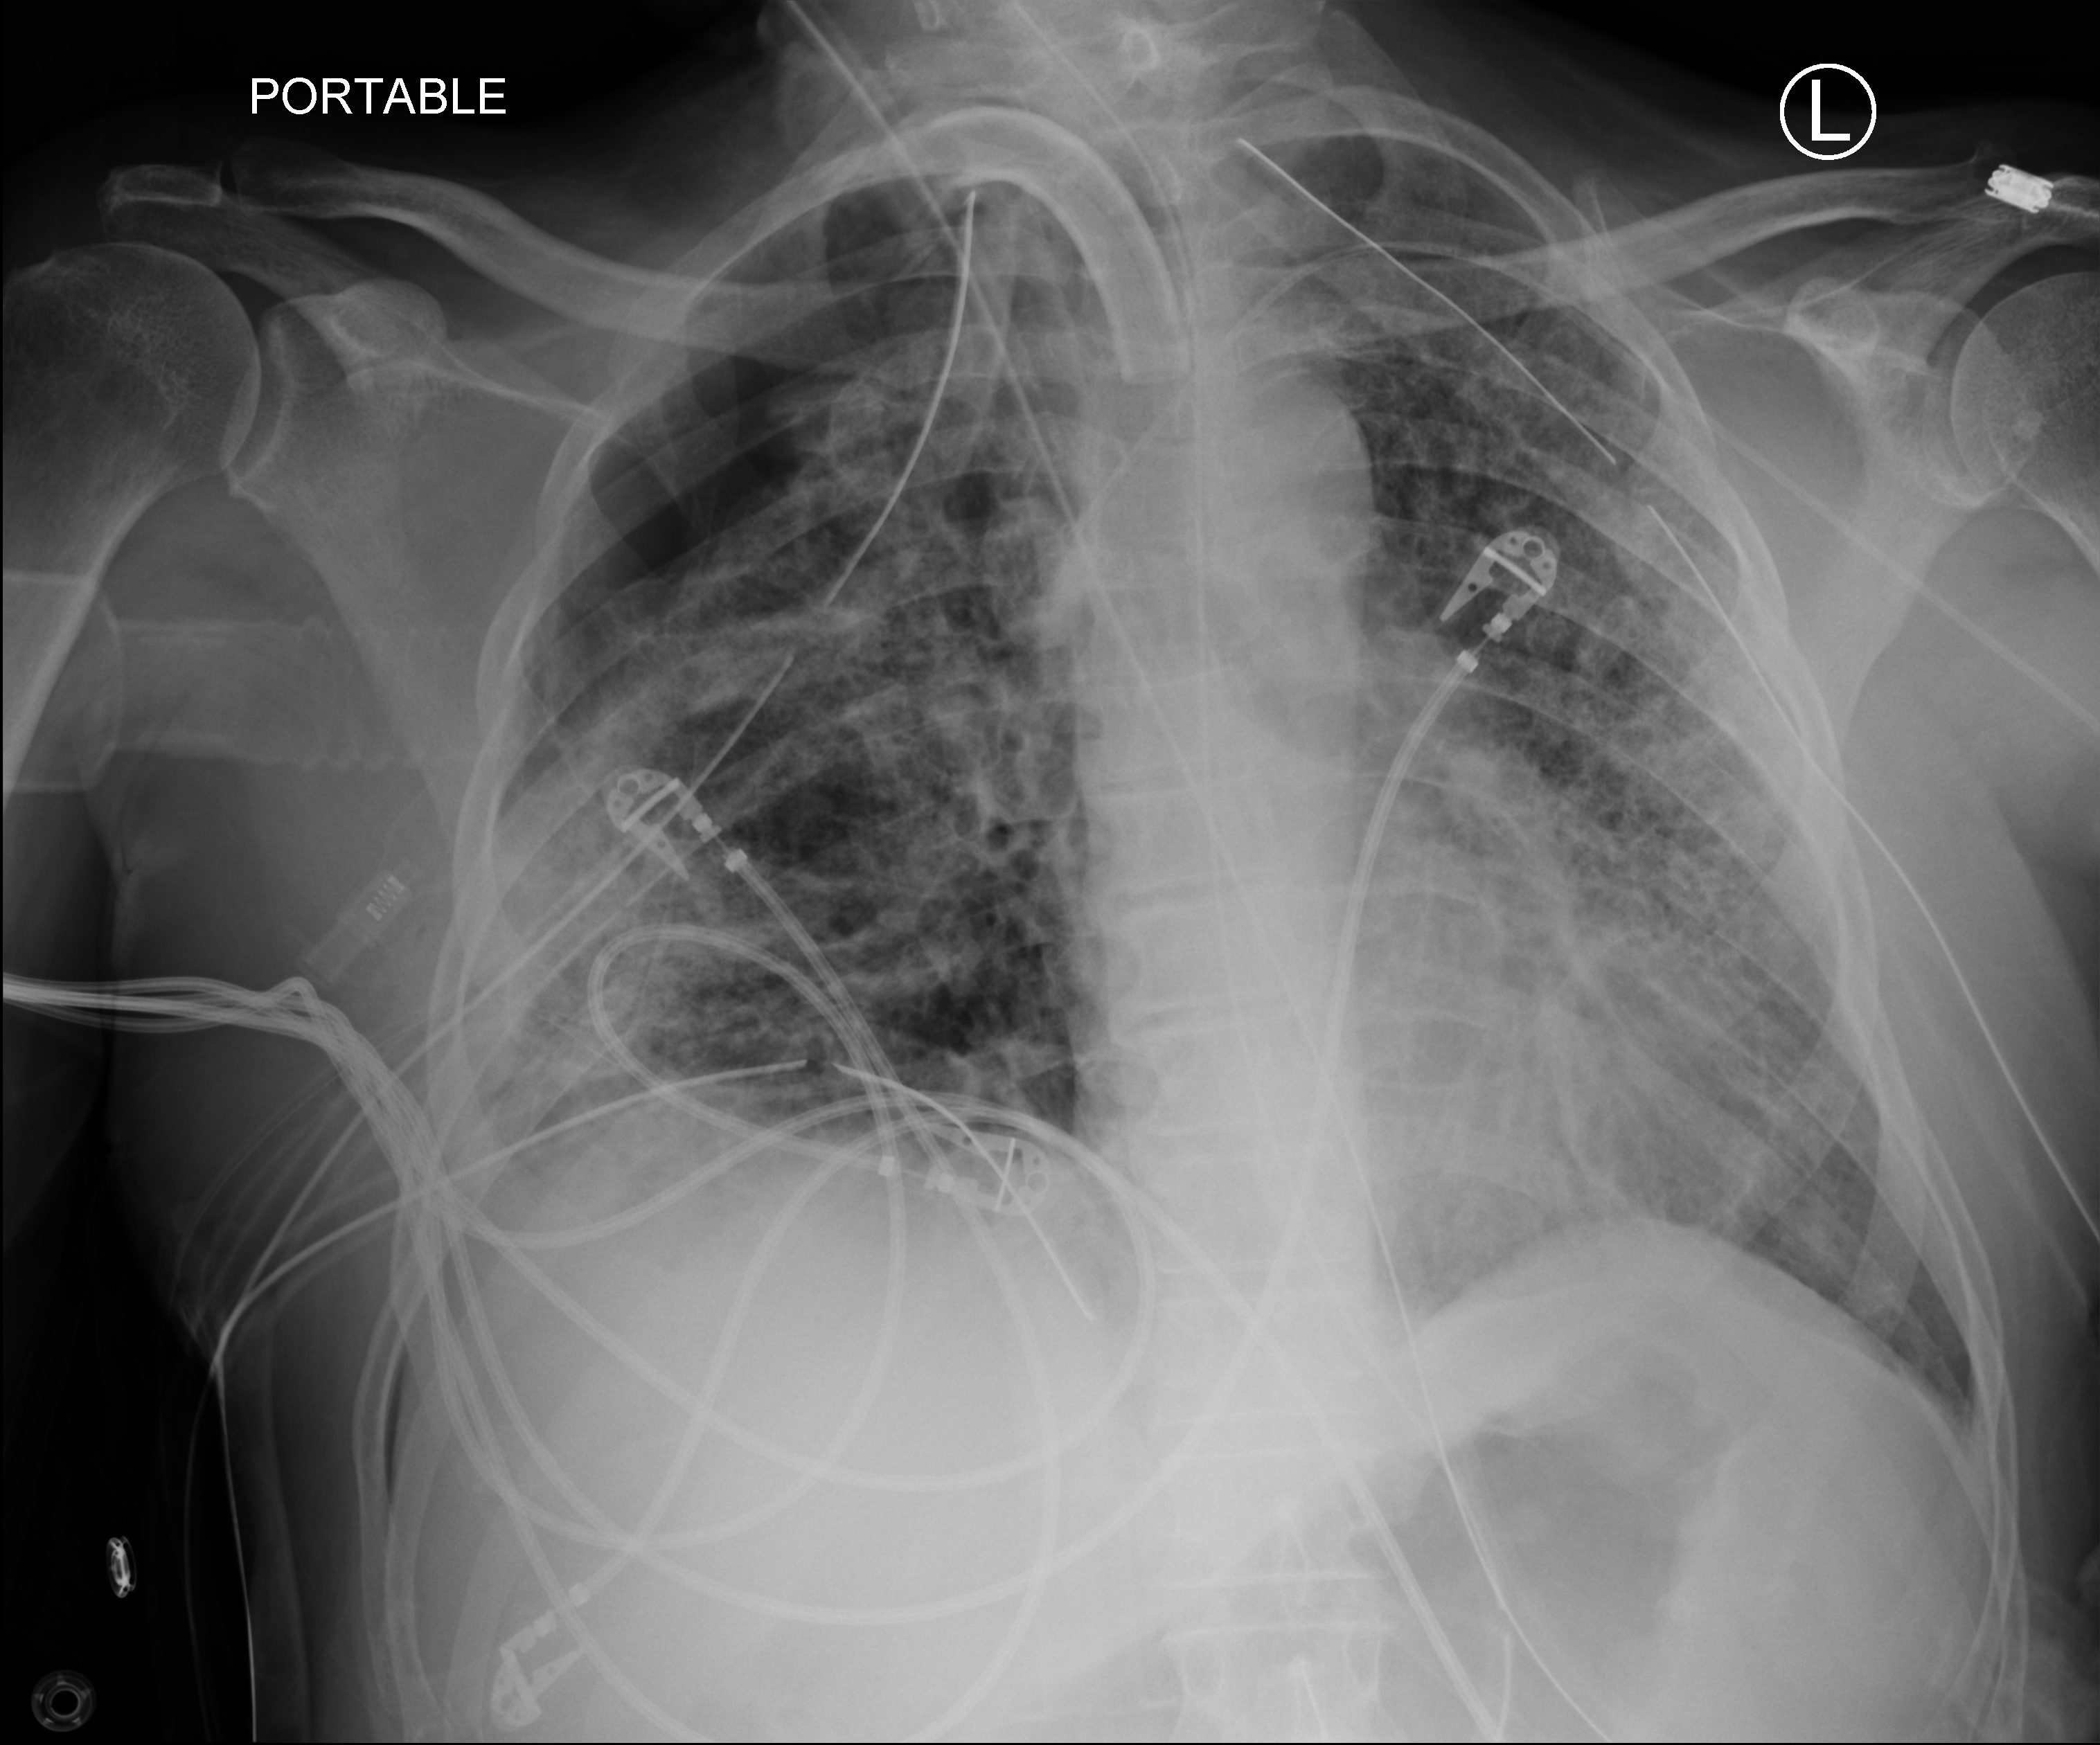
Bedside chest radiograph (computed radiography), anteroposterior (AP) projection. Patient hospitalised with COVID-19; male, aged 18–59 years.
Hospital-stay facts (about this admission, not read from this image; timing relative to this image not recorded): diabetes (admission record): no; admitted to intensive care during this hospital stay: yes; mechanically ventilated during this hospital stay: yes.